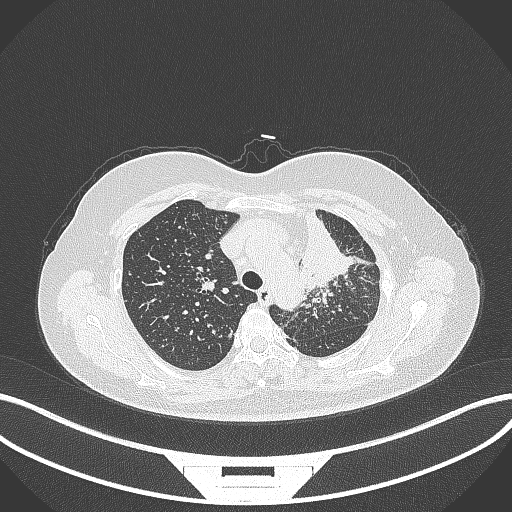
Chest CT, one axial slice. Reconstruction kernel B70f. 120 kVp. Lung window (W 1500 / L -600 HU). 512 × 512 image matrix, field of view 400 × 400 mm. Patient: female, 49 years. From the clinical record (not read from this slice): clinical TNM (as recorded): T1c N0 M1.
Structures marked on this image (rectangle marked by the reading radiologist):
- lung tumour (recorded histology: adenocarcinoma): box from (x=297, y=209) to (x=356, y=288) px